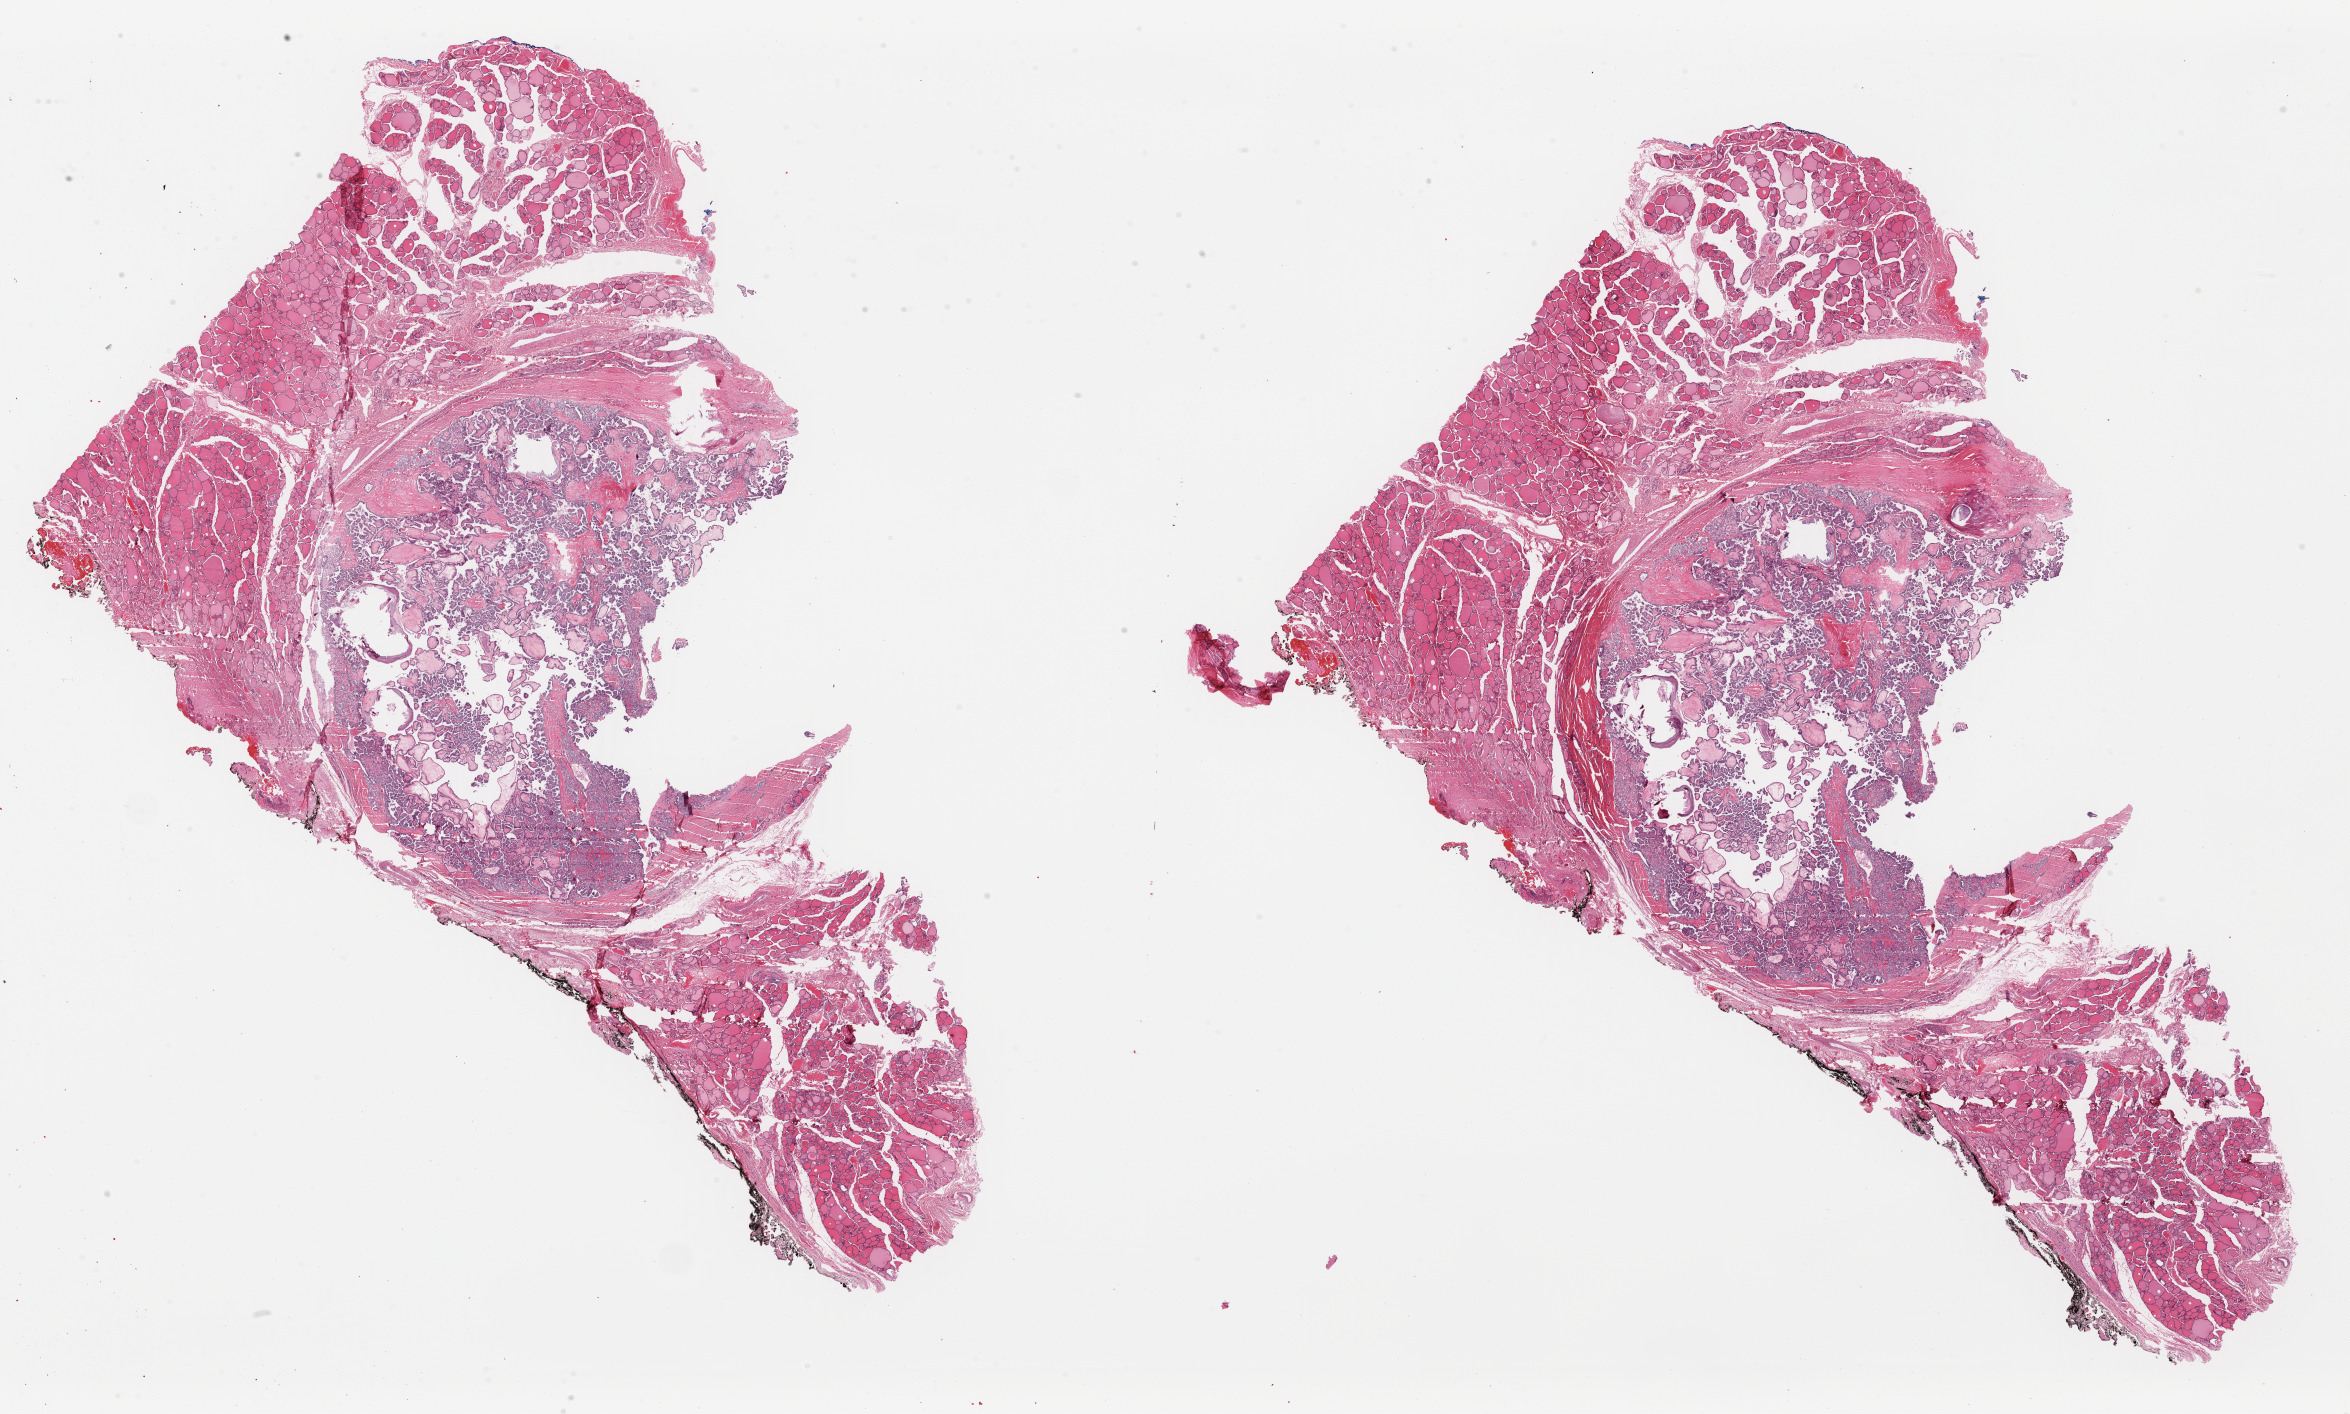
Whole-slide histology image, H&E-stained — a low-resolution overview of the entire scanned area, about 37.1 x 22.3 mm; formalin-fixed paraffin-embedded (FFPE) diagnostic section; primary tumour sample from the thyroid. Patient: male, age at initial diagnosis 50 years.
AJCC pathologic stage: I. Diagnosis: Papillary adenocarcinoma, NOS (thyroid gland). TNM: T1b N0 M0. Laterality: left.